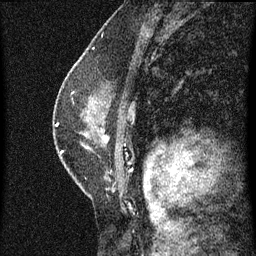
Breast MRI (dynamic contrast-enhanced), one sagittal slice; dynamic contrast-enhanced series, image 2 of 3 at this slice position (ordered by acquisition); 1.5 T; TE 4.2 ms, TR 8 ms; 256 × 256 image matrix. Female patient, age 47 years.
Structures marked on this image (semi-automatically segmented with operator editing):
- analysis volume of interest (the breast-tissue region the enhancement analysis was run in; not a lesion): box from (x=54, y=80) to (x=134, y=187) px
- tumour enhancement mask (voxels above the 70 % enhancement threshold inside the analysis volume of interest): (x=57, y=124)–(x=64, y=155)